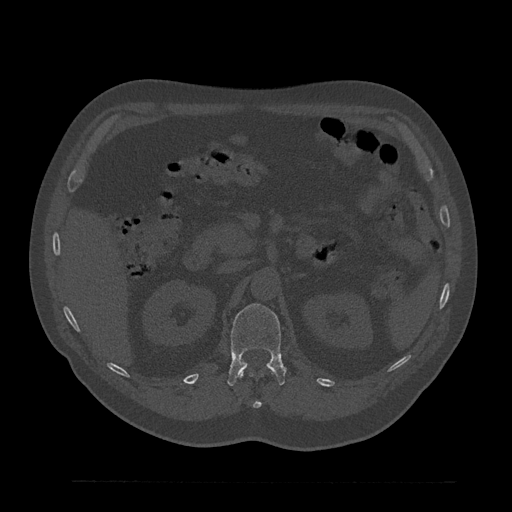
CT including the spine, one axial slice. Position 185 of 797 along the scan axis. Reconstruction kernel Br40s/3. 120 kVp. Bone window (W 1800 / L 400 HU). 512 × 512 image matrix, field of view 430 × 430 mm. Patient: male, 61 years. Case-level facts recorded for this patient, not image findings: primary cancer: prostate.
Structures marked on this image (semi-automatic segmentation, software-assisted and operator-edited):
- L1 vertebra: bounding box [x1, y1, x2, y2] px = [227, 304, 286, 386]
- T12 vertebra: [240, 372, 273, 409]